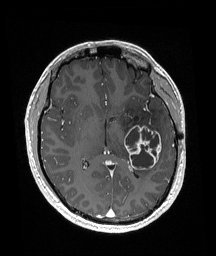
Brain MRI from a brain-tumour surgery series, one axial slice; slice 94 of 192 in the series (ordered by position); T1-weighted post-contrast; 1 mm slice thickness; 216 × 256 image matrix. Case-level facts recorded for this patient, not image findings: histopathology: Glioneuronal tumor; WHO grade: 2; tumour location: Left Superior Temporal Gyrus.
Structures marked on this image (manually delineated by an expert):
- tumour: box from (x=124, y=125) to (x=162, y=170) px